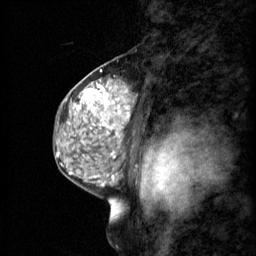
Breast MRI (dynamic contrast-enhanced), one sagittal slice. Slice 38 of 60 in the series (ordered by position). 3 images stored at this slice position (order not interpretable as contrast timing). 1.5 T. TE 4.2 ms, TR 11 ms. 2 mm slice thickness. 256 × 256 image matrix, field of view 200 × 200 mm. Female patient, age 48 years.
Structures marked on this image (semi-automatic segmentation, software-assisted and operator-edited):
- analysis volume of interest (the breast-tissue region the enhancement analysis was run in; not a lesion): box from (x=69, y=74) to (x=133, y=147) px
- tumour enhancement mask (voxels above the 70 % enhancement threshold inside the analysis volume of interest): (x=69, y=80)–(x=131, y=143)